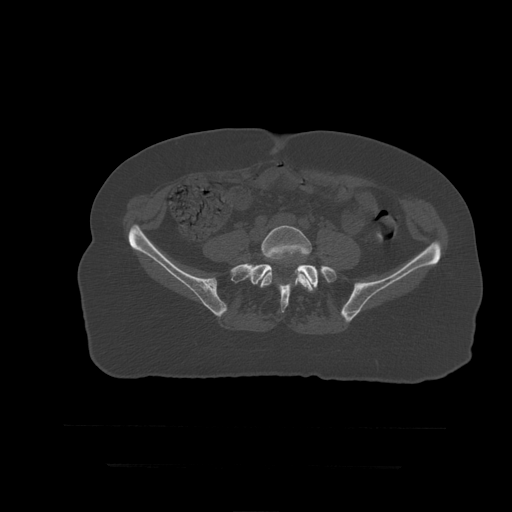
CT including the spine, one axial slice. Slice 63 of 399 in the series (ordered by position). Reconstruction kernel STANDARD. Bone window (W 1800 / L 400 HU). 1.25 mm slice thickness. 512 × 512 image matrix, field of view 450 × 450 mm. Patient age 41 years. From the clinical record (not read from this slice): primary cancer: breast.
Annotated regions visible in this slice (semi-automatic segmentation, software-assisted and operator-edited):
- L5 vertebra: box from (x=260, y=226) to (x=314, y=292) px